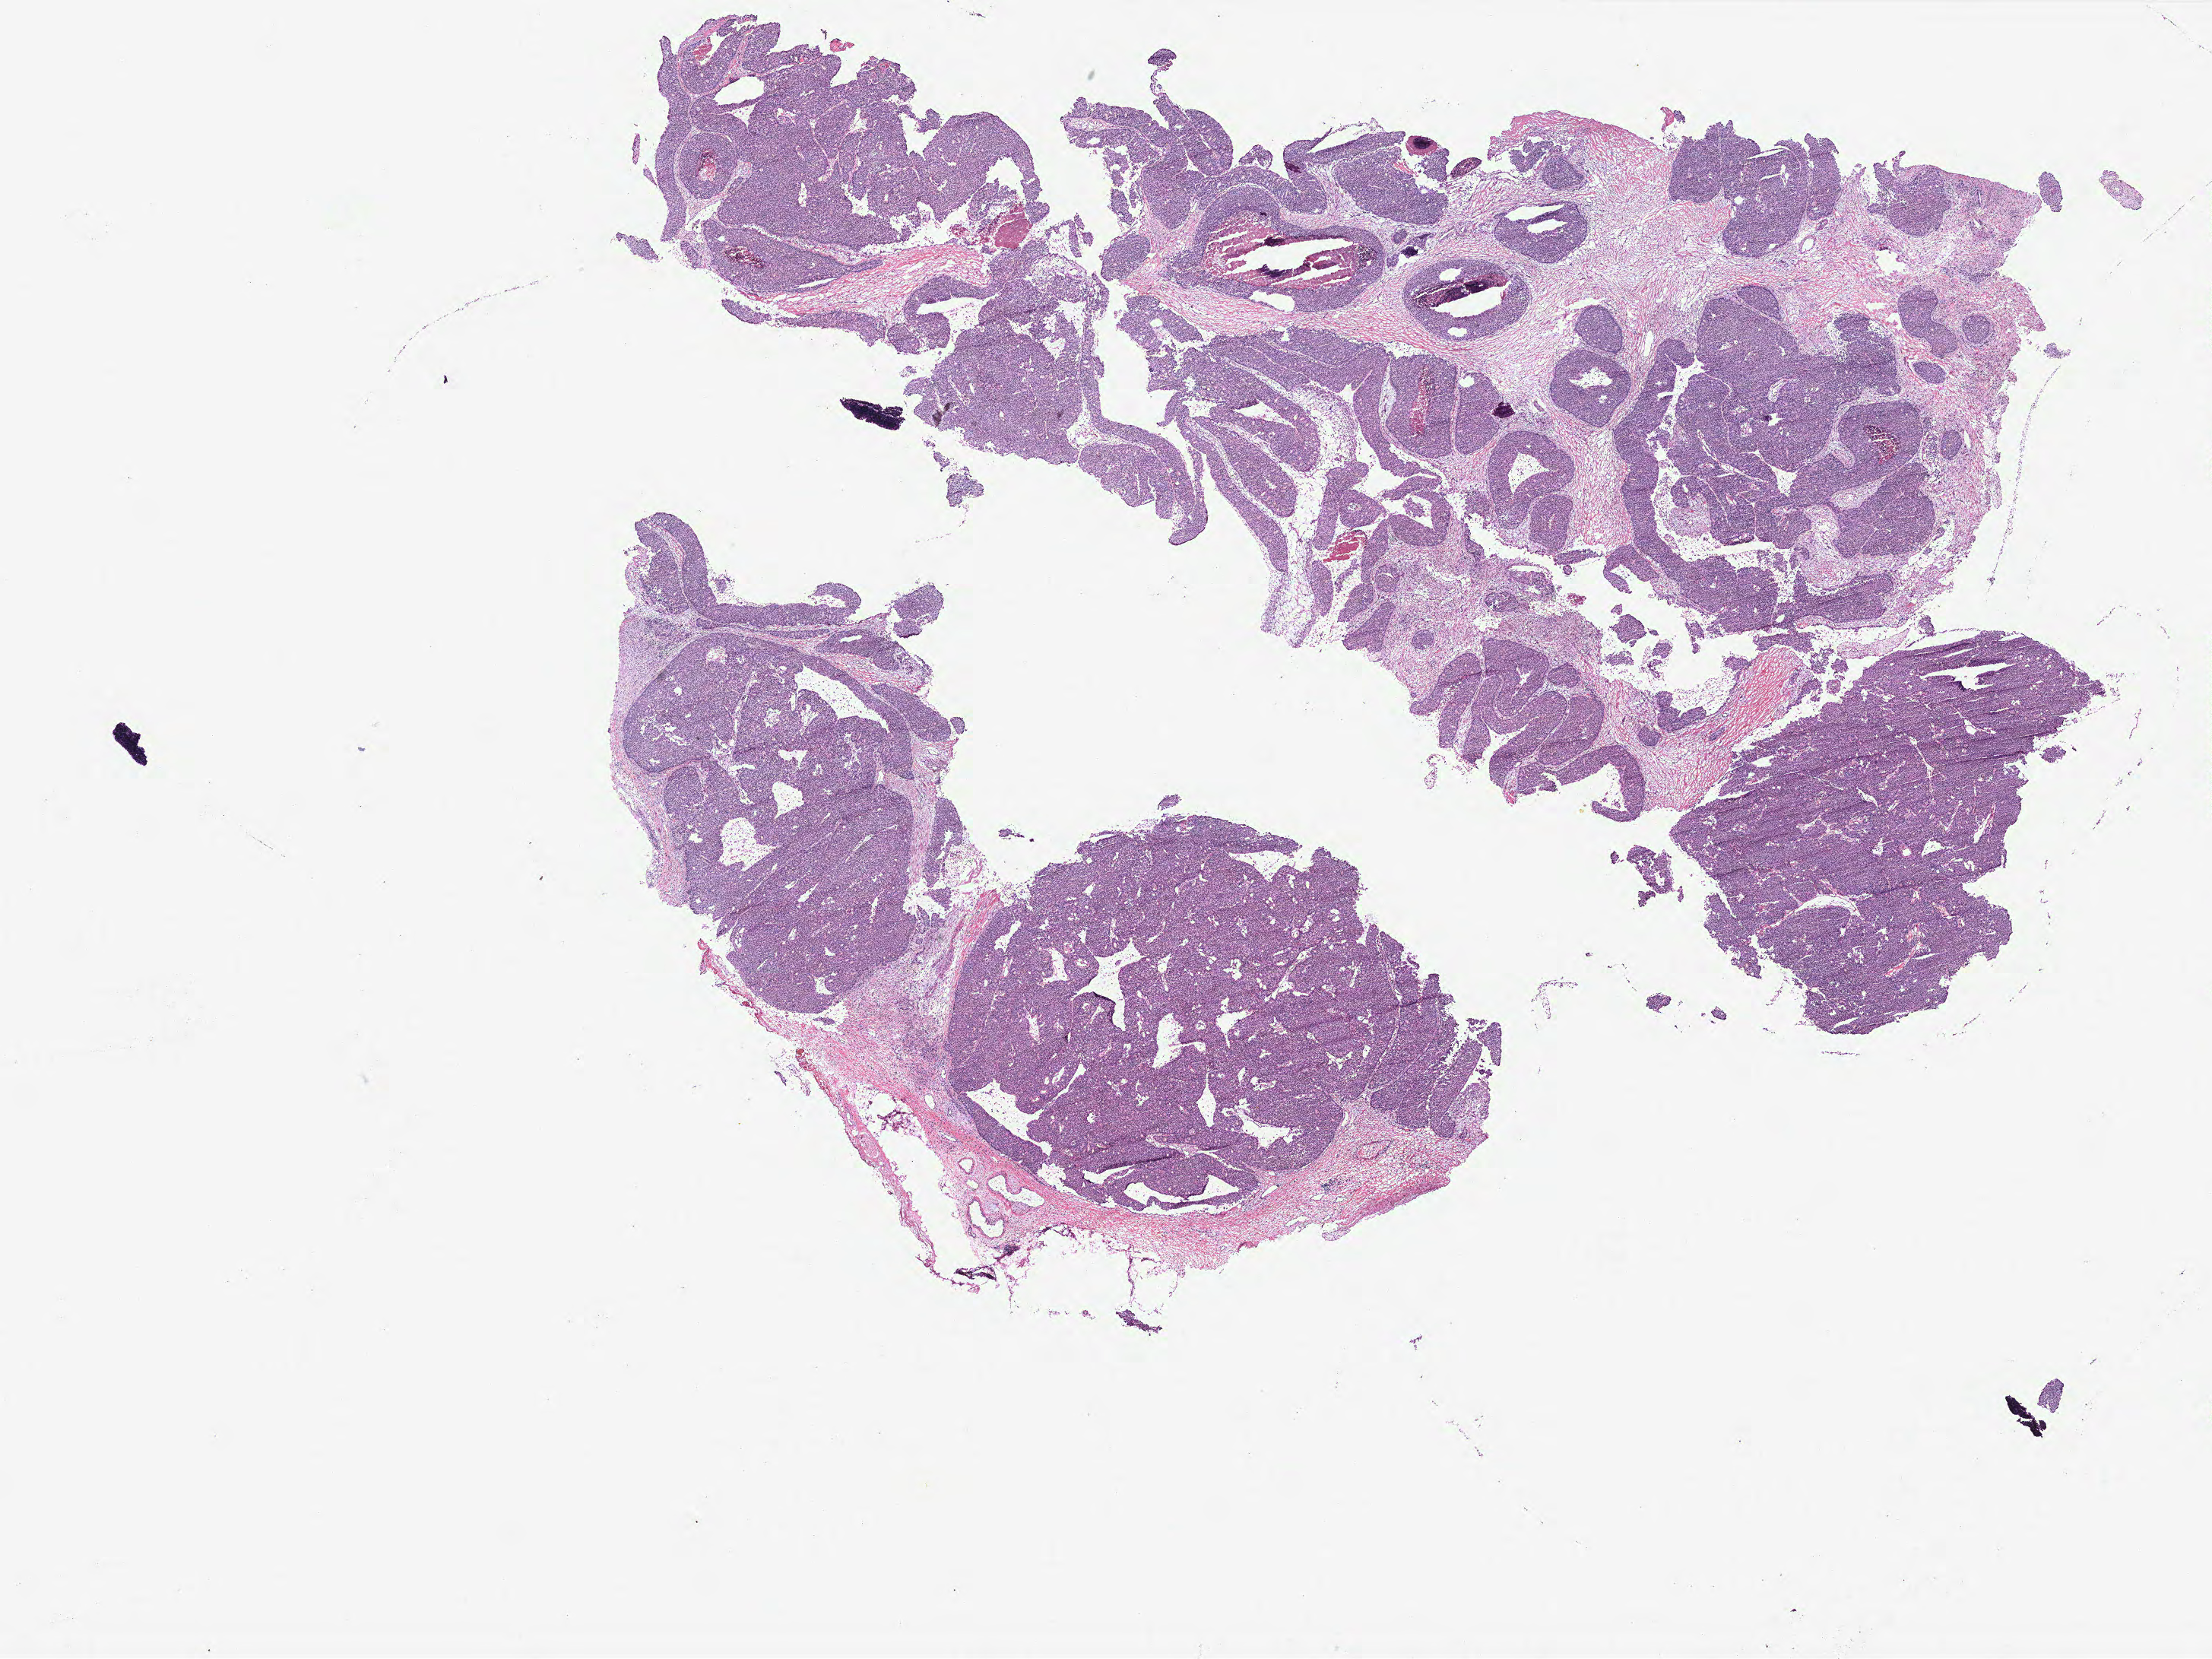
Digitized H&E-stained tissue section (whole slide), a low-resolution overview of the entire scanned area, about 23.3 x 17.5 mm (slide scanned at 40x). Breast, tissue type not recorded. Patient: female, age 41 years.
* patient diagnosis: Infiltrating duct carcinoma, NOS